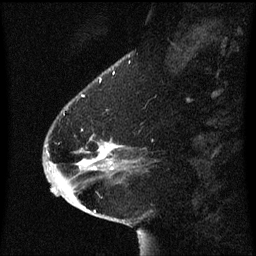
Breast MRI (dynamic contrast-enhanced), one sagittal slice. Position 17 of 60 along the scan axis. Dynamic contrast-enhanced series, image 2 of 3 at this slice position (ordered by acquisition). 1.5 T. TE 4.2 ms, TR 8.4 ms. 2 mm slice thickness. 256 × 256 image matrix. Patient: female, 54 years. Case-level facts recorded for this patient, not image findings: setting: breast cancer imaged before/during neoadjuvant chemotherapy; receptor status: HR-positive, HER2-negative.
Annotated regions visible in this slice (semi-automatically segmented with operator editing):
- analysis volume of interest (the breast-tissue region the enhancement analysis was run in; not a lesion): bounding box <46,104,123,171> (left, top, right, bottom; pixels)
- tumour enhancement mask (voxels above the 70 % enhancement threshold inside the analysis volume of interest): <101,148,116,163>